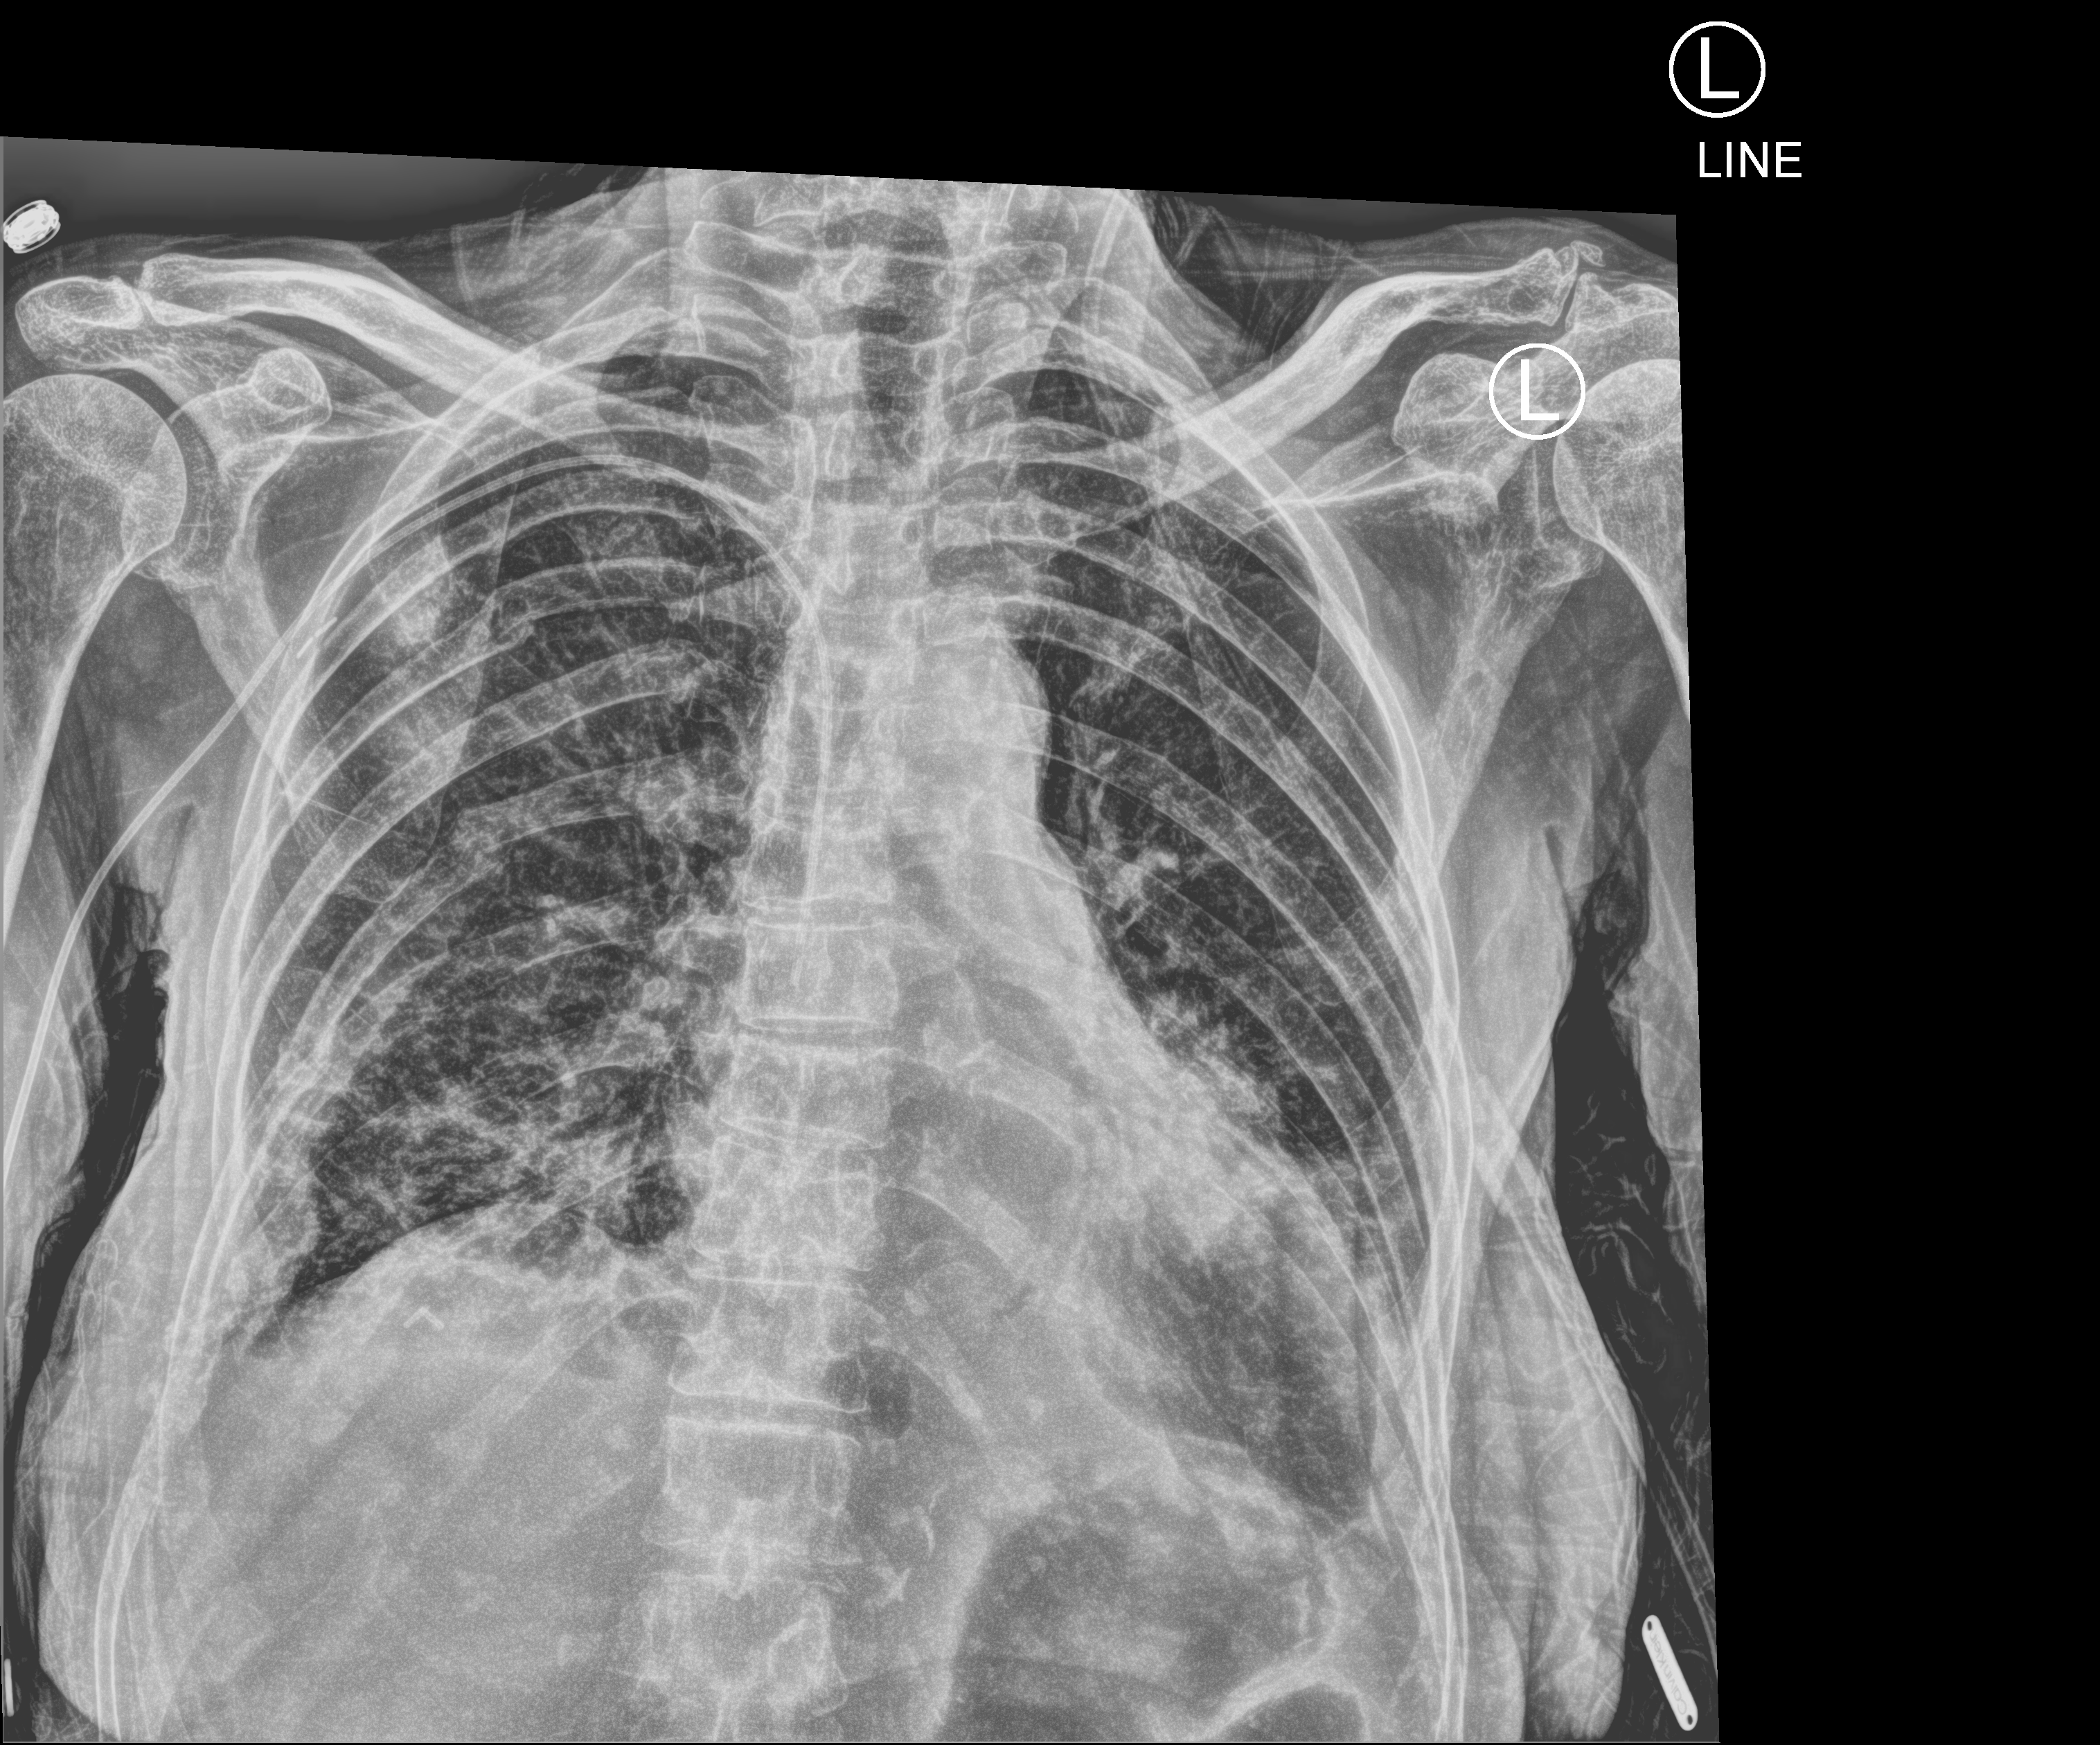
Bedside chest radiograph (computed radiography), anteroposterior (AP) projection. Female patient hospitalised with COVID-19, age 60–74 years.
Admission-level facts for this patient (not findings on this image; timing relative to this image not recorded): mechanically ventilated during this hospital stay: no; length of hospital stay: 8 days.